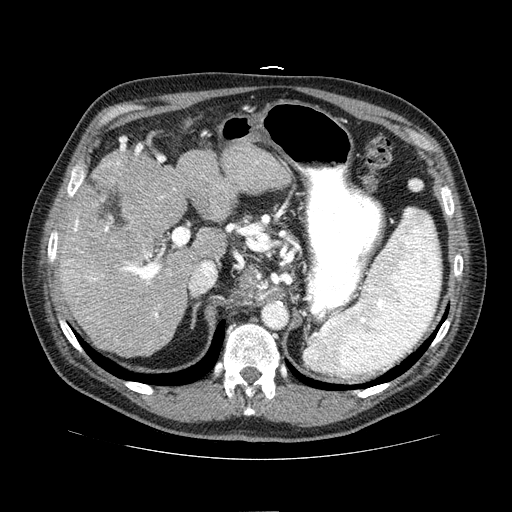
Contrast-enhanced abdominal CT (liver protocol), one axial slice. Position 46 of 81 along the scan axis. 100 kVp. One of 2 acquisitions stored at this slice position. Soft-tissue window (W 400 / L 40 HU). 2.5 mm slice thickness. 512 × 512 image matrix, field of view 400 × 400 mm. From the clinical record (not read from this slice): diagnosis: hepatocellular carcinoma (patient treated with transarterial chemoembolisation; whether this scan precedes or follows treatment is not stated here); TNM stage (as recorded): Stage-IIIA; Child-Pugh class: A; tumour nodularity: multinodular; tumour size: 5.6 cm.
Structures marked on this image (semi-automatic segmentation, software-assisted and operator-edited):
- liver parenchyma outside the tumour (the mass and vessels are separate outlines, so this box may not span the whole liver): bounding box (x1, y1, x2, y2) in pixels: (58, 140, 290, 356)
- liver vessels: (65, 161, 259, 318)